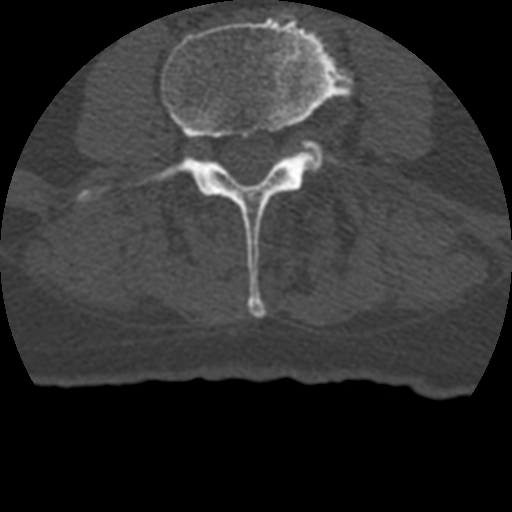
CT including the spine, one axial slice; slice 87 of 399 in the series (ordered by position); reconstruction kernel STANDARD; bone window (W 1800 / L 400 HU); 1.25 mm slice thickness; 512 × 512 image matrix, field of view 160 × 160 mm. Patient age 69 years. From the clinical record (not read from this slice): primary cancer: prostate.
Annotated regions visible in this slice (semi-automatically segmented with operator editing):
- L3 vertebra: box from (x=81, y=14) to (x=354, y=318) px